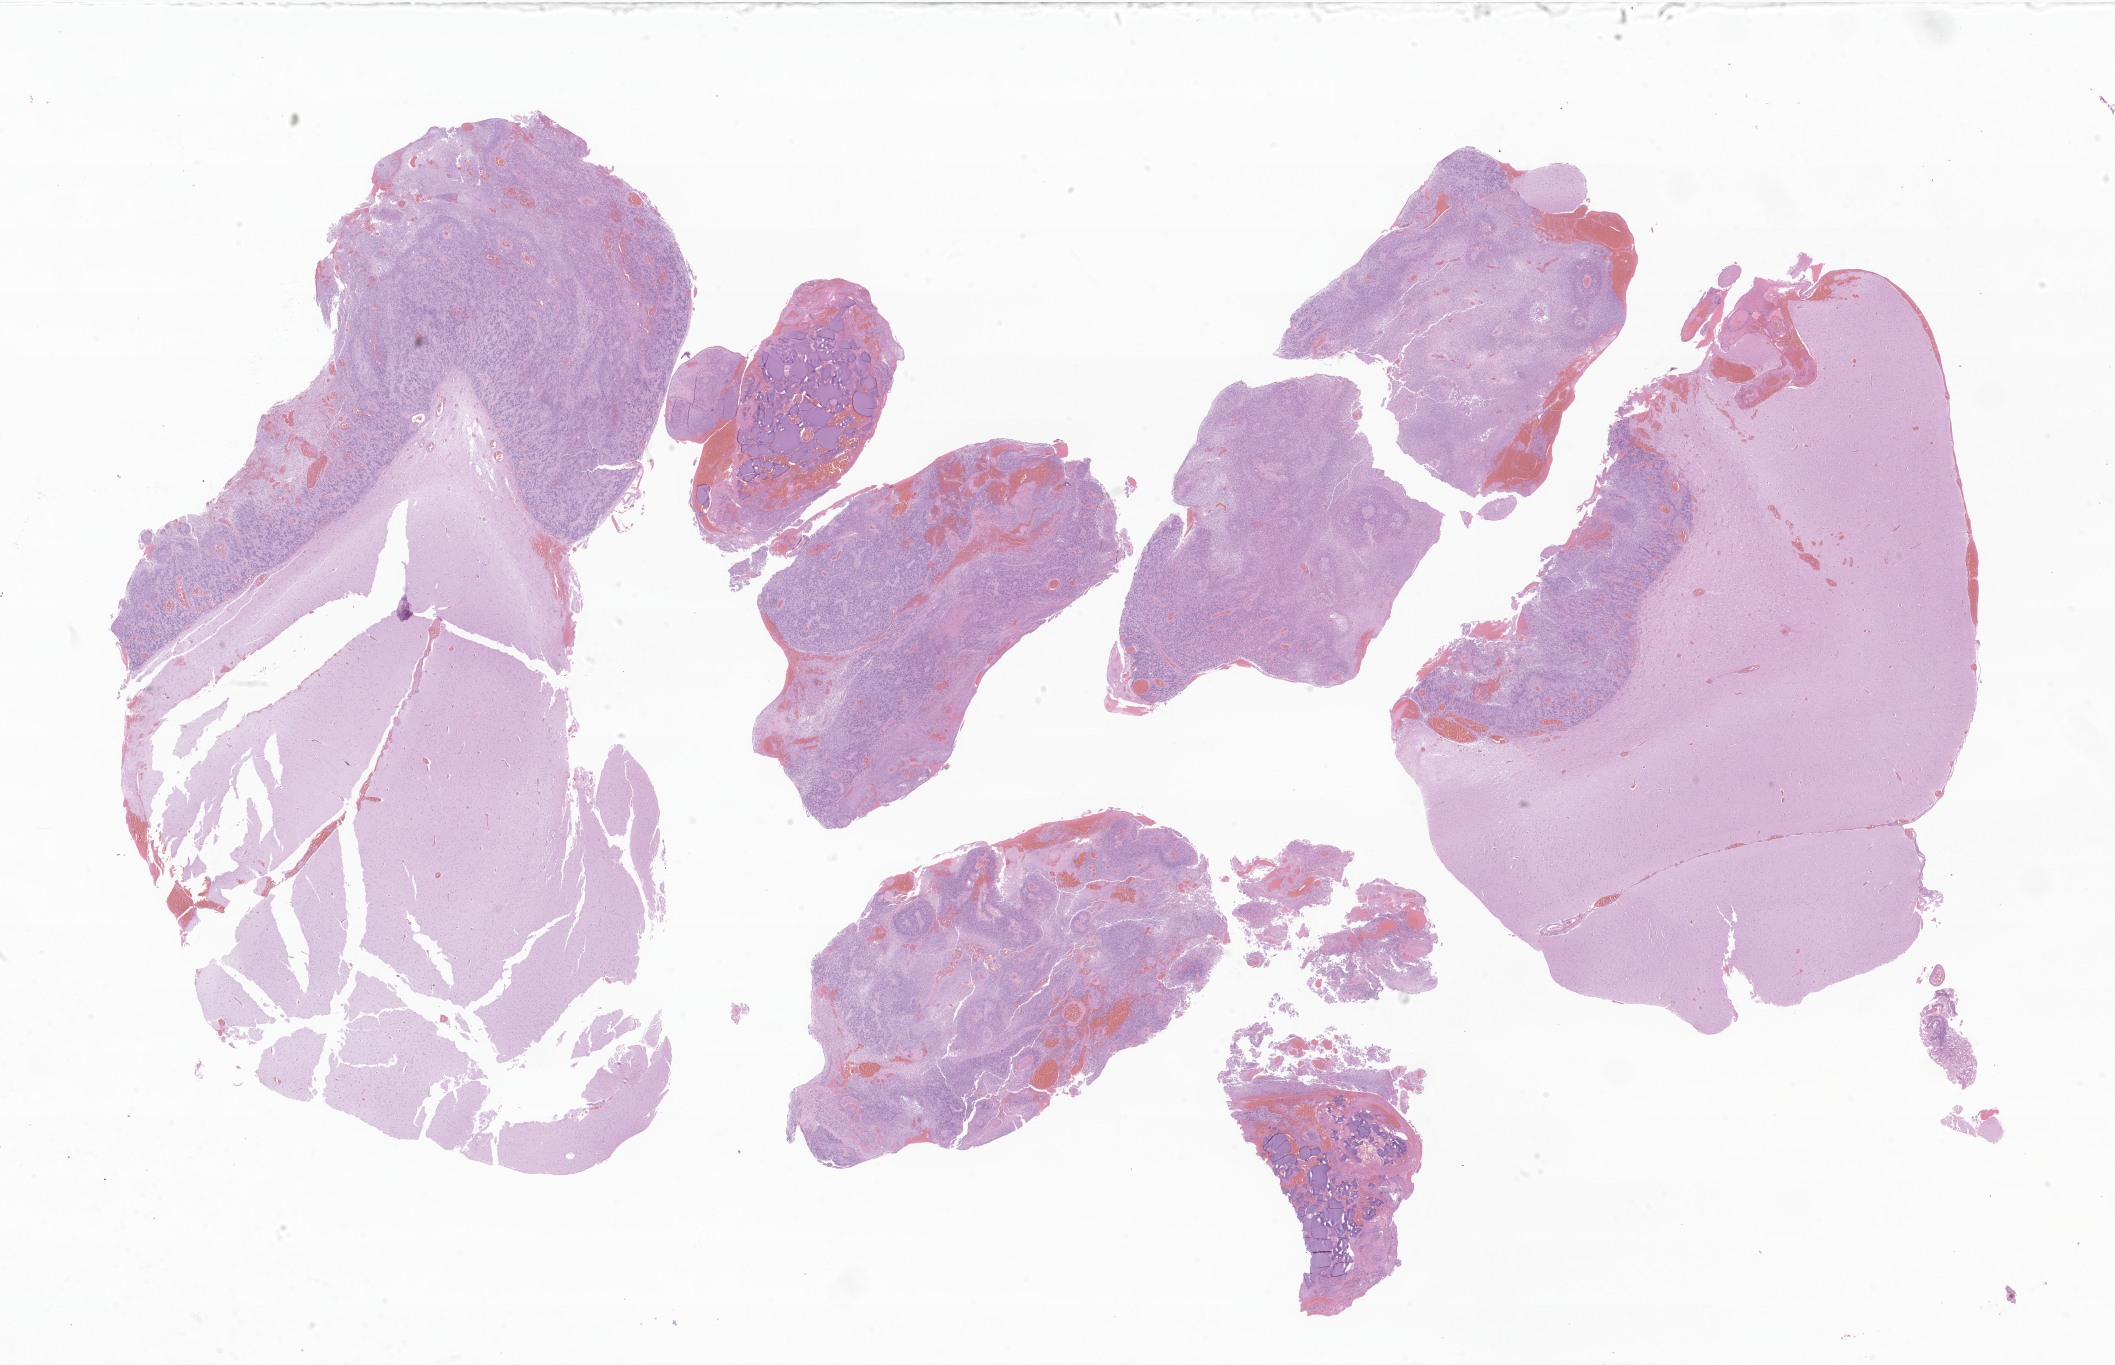
Whole-slide image, haematoxylin and eosin stain of tumor tissue from the brain — low-resolution overview of the scanned area, about 35.7 x 23.0 mm, formalin-fixed, paraffin-embedded (FFPE) tissue. Patient female; age 602 days (about 1.6 years).
Diagnosis: Ependymoma, NOS.